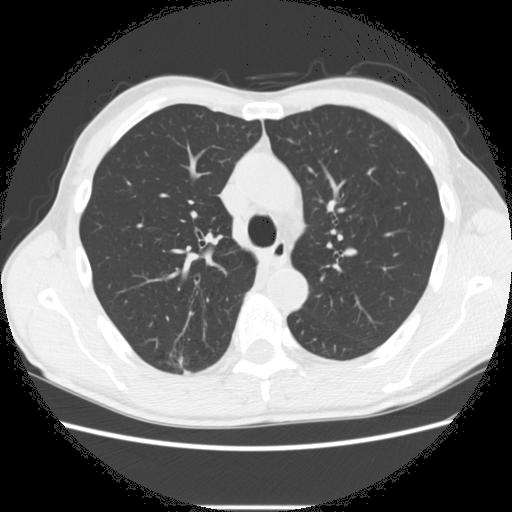
Axial slice from a low-dose chest CT screening exam, second annual screen, lung window (W 1500 / L -600 HU), 2.5 mm slice thickness, slice 88 of 282 in the series, 512 × 512 image matrix. Male, age 66 years at enrolment.
Expert-annotated lung lesion, bounding box <165,343,219,385> (left, top, right, bottom; pixels). The screening reader recorded 5 non-calcified nodules or masses ≥4 mm on this exam (right lower lobe, right upper lobe, right upper lobe, right upper lobe, left lower lobe); which of them this box marks is not recorded. Later outcome: lung cancer diagnosed 75 days after this screen — adenocarcinoma, NOS, right upper lobe, undifferentiated (G4), stage IA (AJCC 6th edition), 20 mm at pathology.